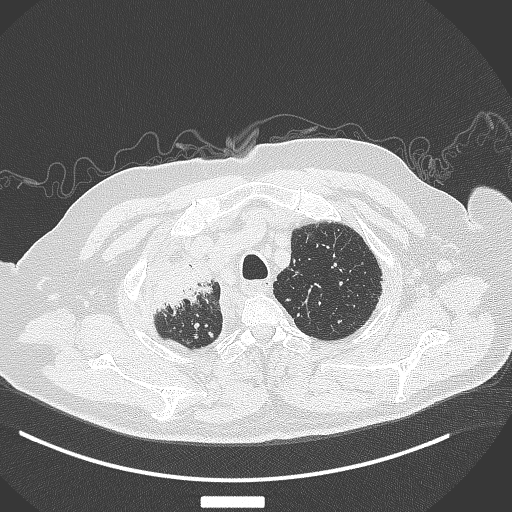
Chest CT, one axial slice. Position 317 of 384 along the scan axis. 120 kVp. Lung window (W 1500 / L -600 HU). 1 mm slice thickness. 512 × 512 image matrix, field of view 400 × 400 mm. Patient: male, 69 years. Case-level facts recorded for this patient, not image findings: clinical TNM (as recorded): T4 N3 M1.
Outlined on this slice (rectangle marked by the reading radiologist):
- lung tumour (recorded histology: adenocarcinoma): bounding box <145,252,215,324> (left, top, right, bottom; pixels)